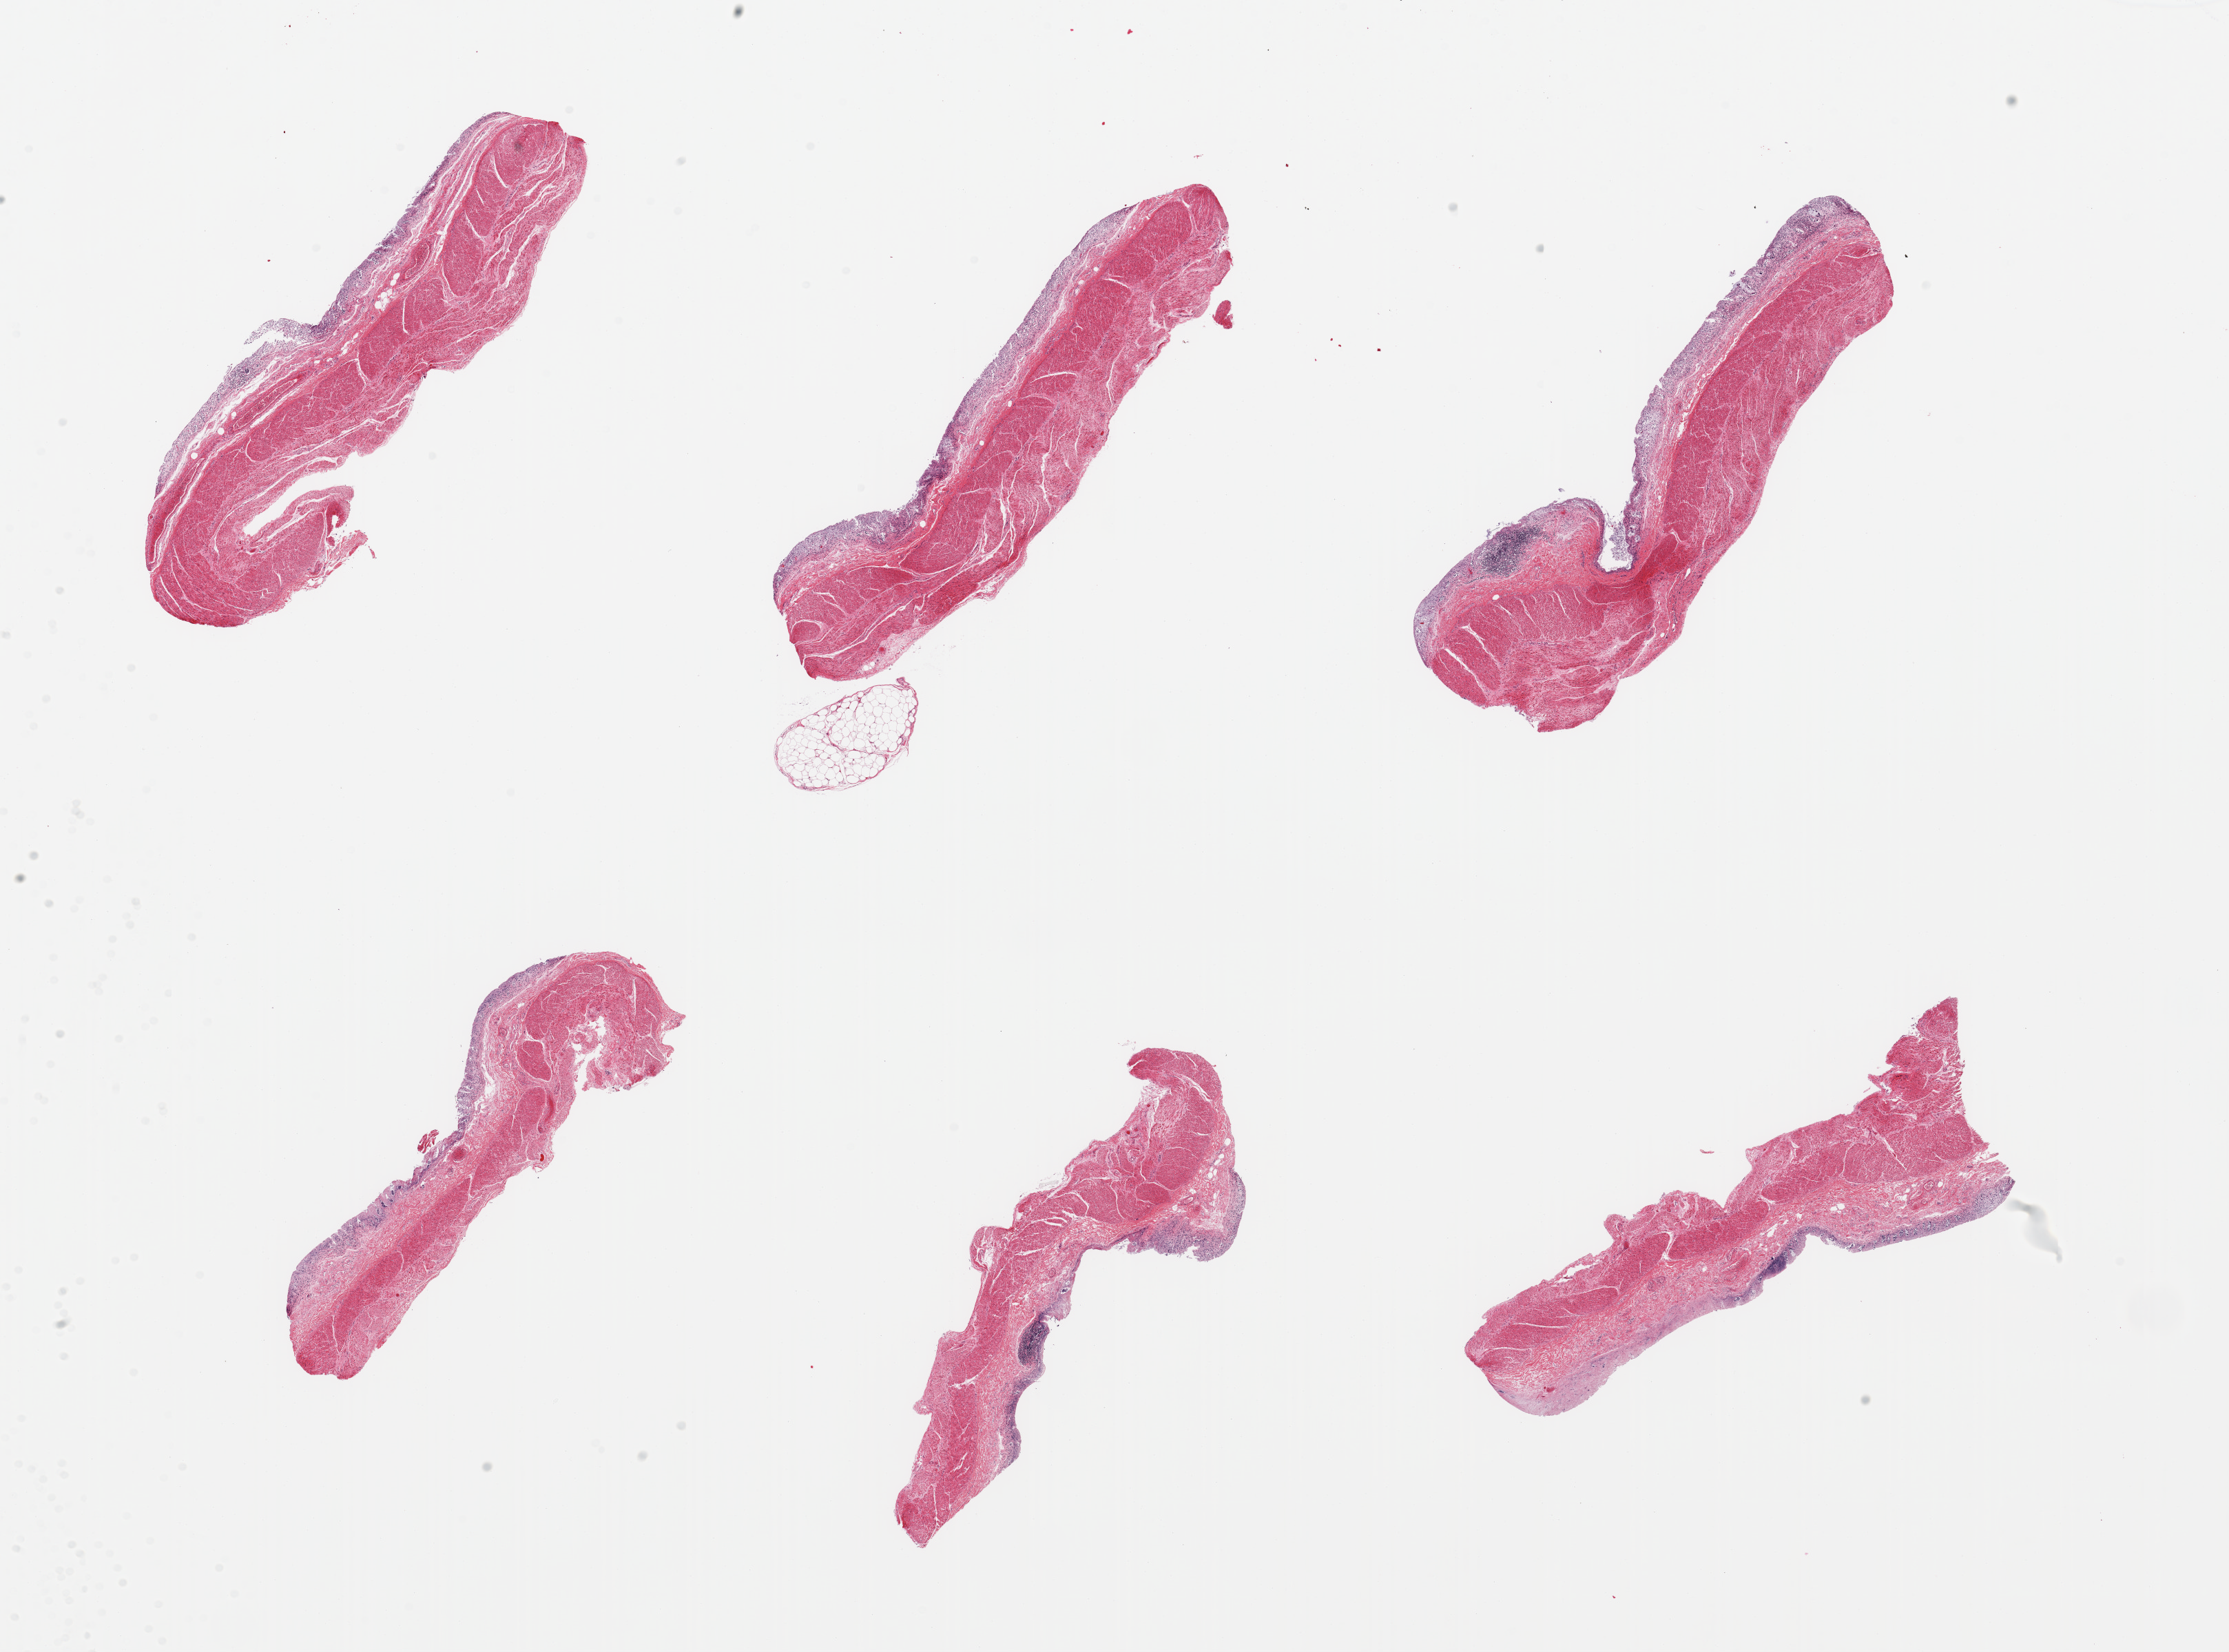
Digitized haematoxylin and eosin-stained section, whole scanned area (about 25.6 x 19.0 mm, from a 20x scan) shown as a low-resolution overview; PAXgene-fixed, paraffin-embedded tissue; target tissue: transverse colon; donor tissue sample.
Pathologist's review note for this sample: 6 pieces; mucosa severely autolyzed; muscle moderately.